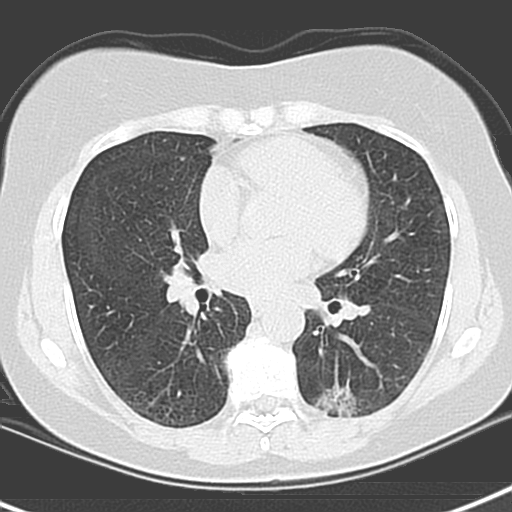
Low-dose screening chest CT, axial slice, baseline screening round, lung window (W 1500 / L -600 HU), 3.2 mm slice thickness, 120 kVp, slice 73 of 129 in the series. Female participant, aged 55 years at enrolment.
Expert-annotated lung lesion, bounding box (x1, y1, x2, y2) in pixels: (311, 374, 387, 423). The screening reader recorded 3 non-calcified nodules or masses ≥4 mm on this exam (left upper lobe, left lower lobe, left lower lobe); which of them this box marks is not recorded. Lung cancer was diagnosed 1063 days after this screen: adenocarcinoma with mixed subtypes, left lower lobe, poorly differentiated (G3), stage IA (AJCC 6th edition), 21 mm at pathology.